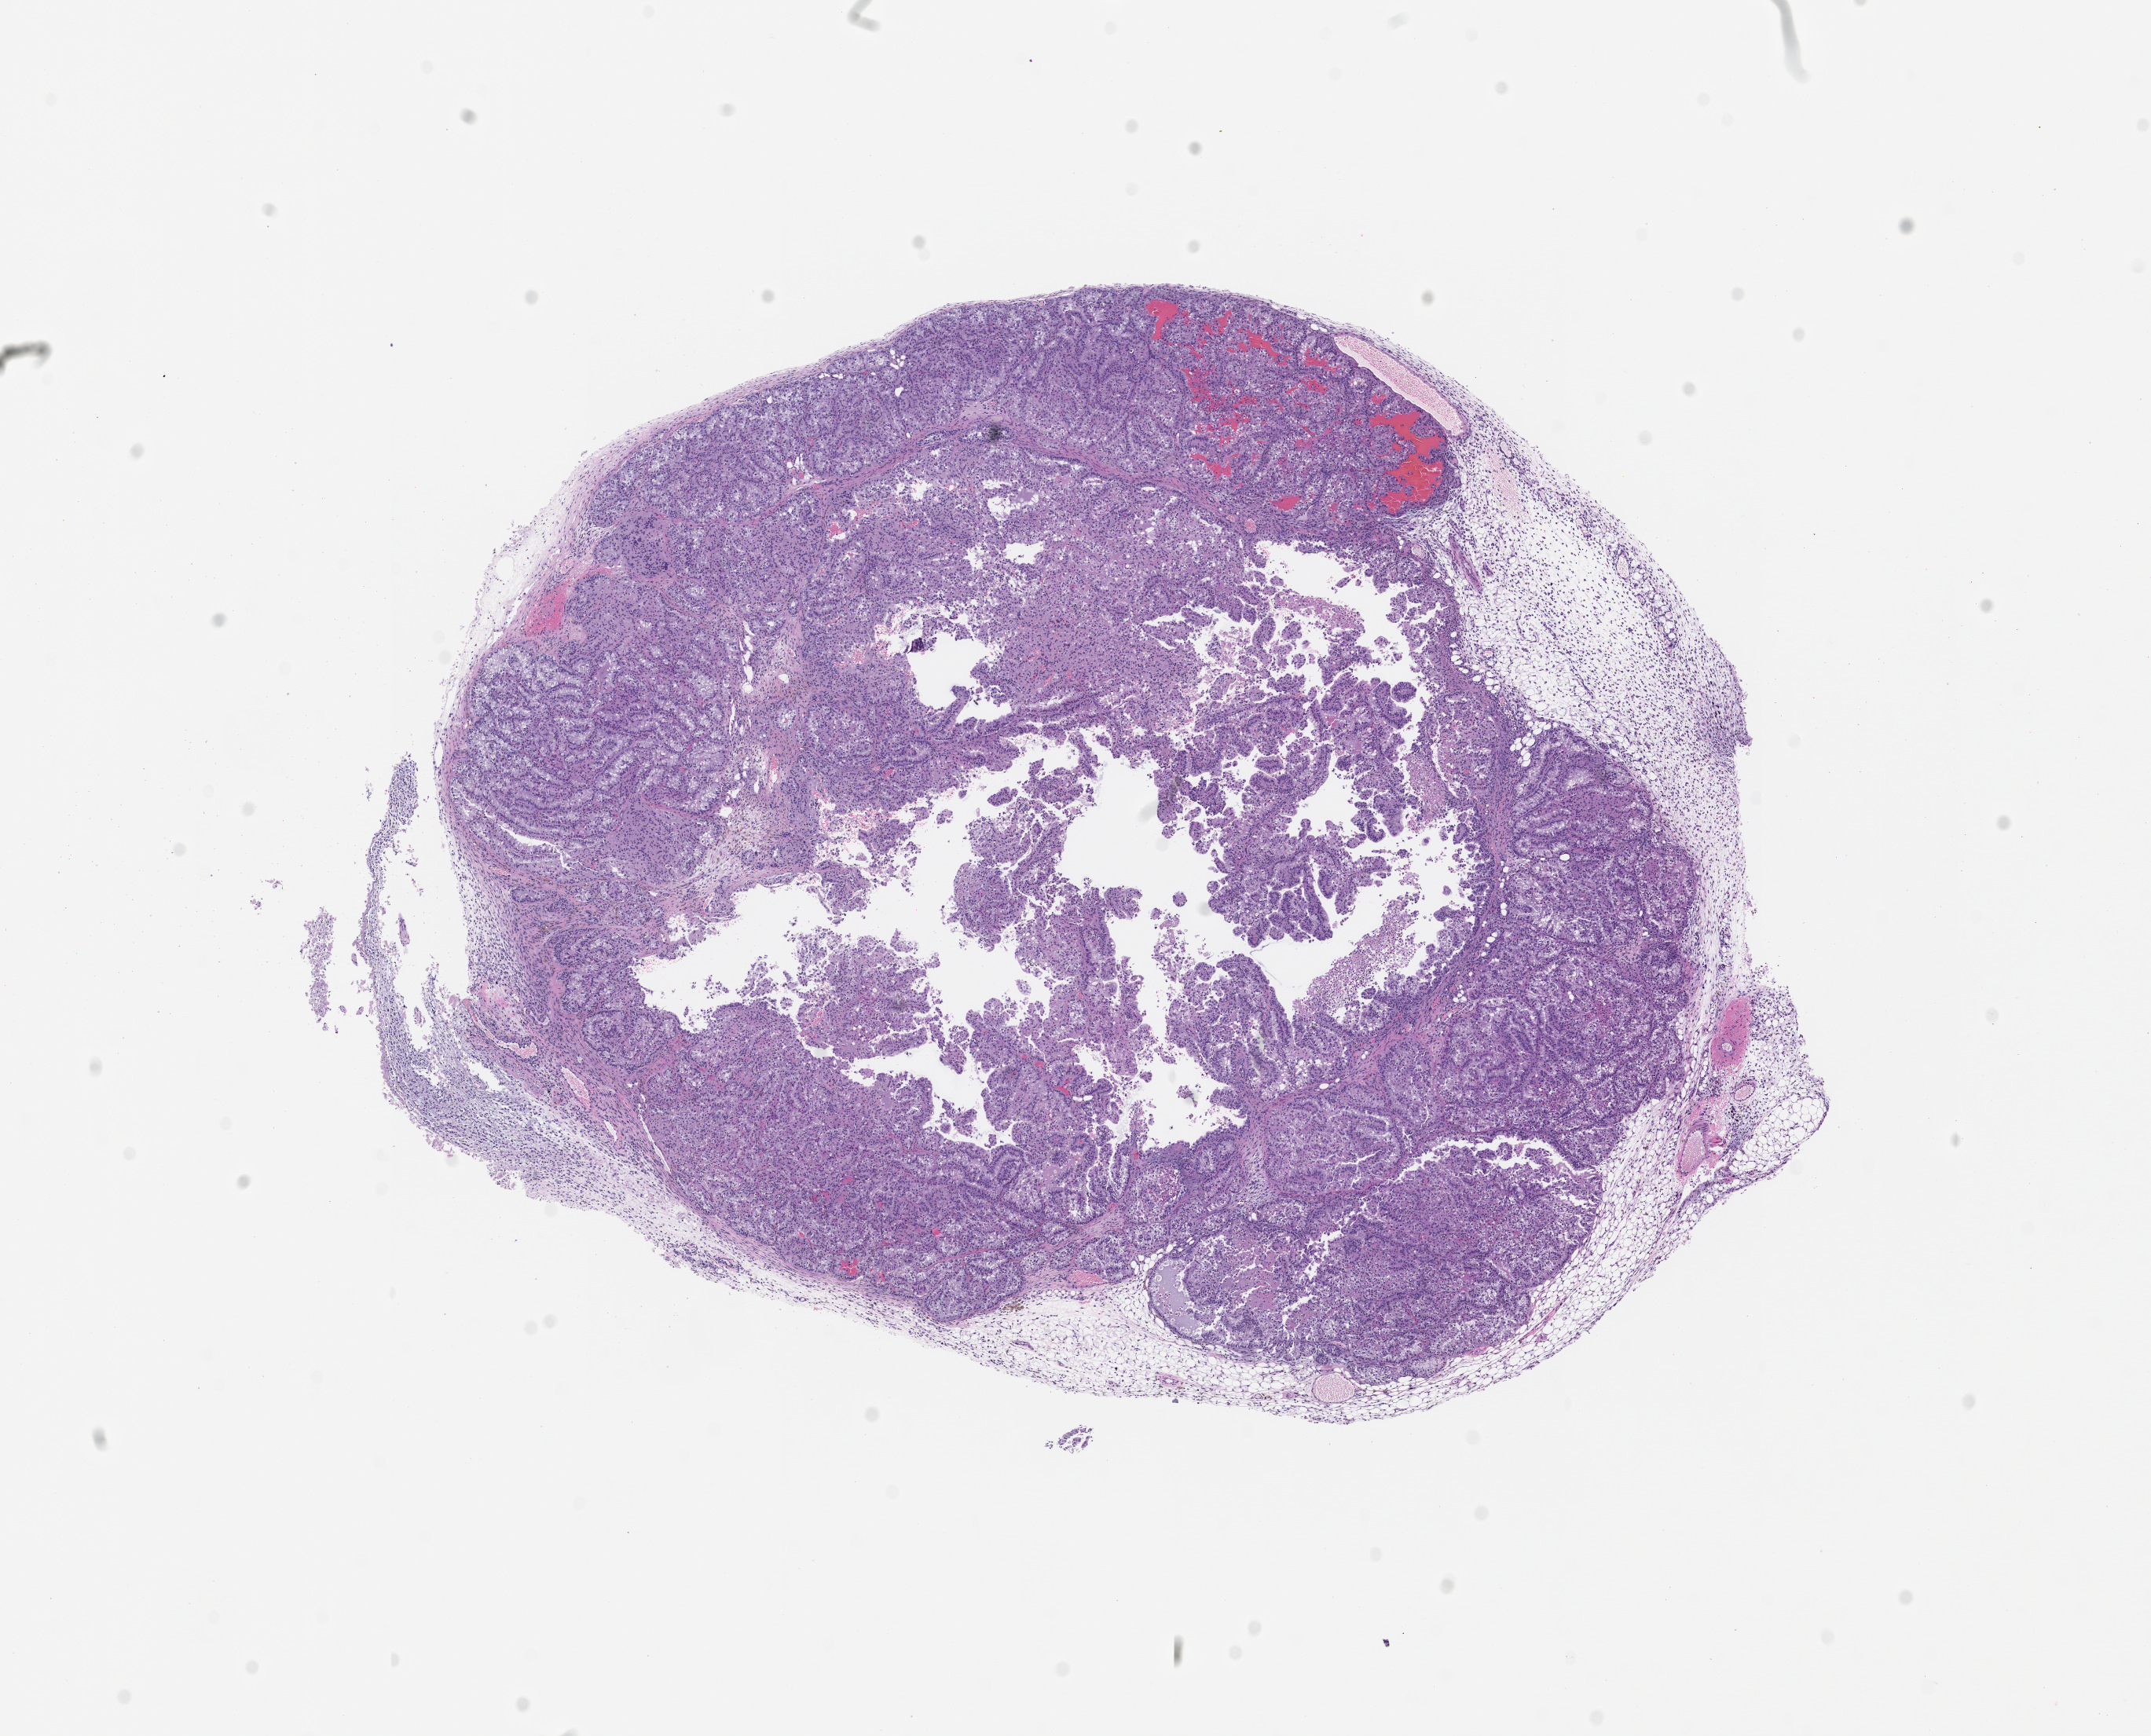
Whole-slide image, haematoxylin and eosin: patient-derived xenograft (human tumor grown in a mouse), passage 2 — low-resolution overview of the scanned area, about 11.0 x 8.9 mm; FFPE section; originating tumor site category: genitourinary tract.
• originating patient diagnosis: Renal Cell Carcinoma, Not Otherwise Specified